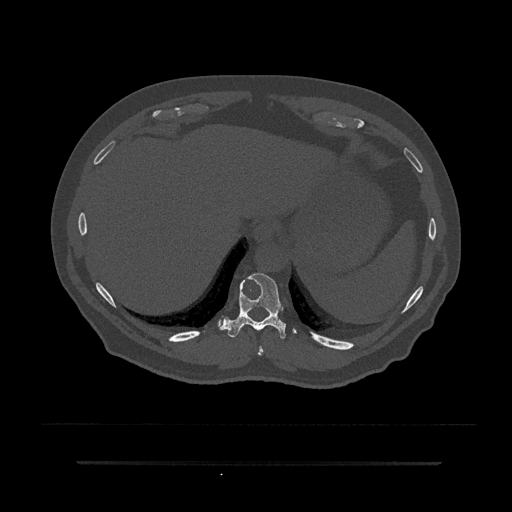
CT including the spine, one axial slice; slice 329 of 797 in the series (ordered by position); 120 kVp; bone window (W 1800 / L 400 HU); 0.5 mm slice thickness; 512 × 512 image matrix. Patient: male, 59 years. Case-level facts recorded for this patient, not image findings: primary cancer: bile ducts; vertebrae with lytic lesions (as recorded): T10.
Structures marked on this image (semi-automatic segmentation, software-assisted and operator-edited):
- T10 vertebra: box from (x=220, y=273) to (x=296, y=339) px
- T9 vertebra: (x=258, y=346)–(x=264, y=356)